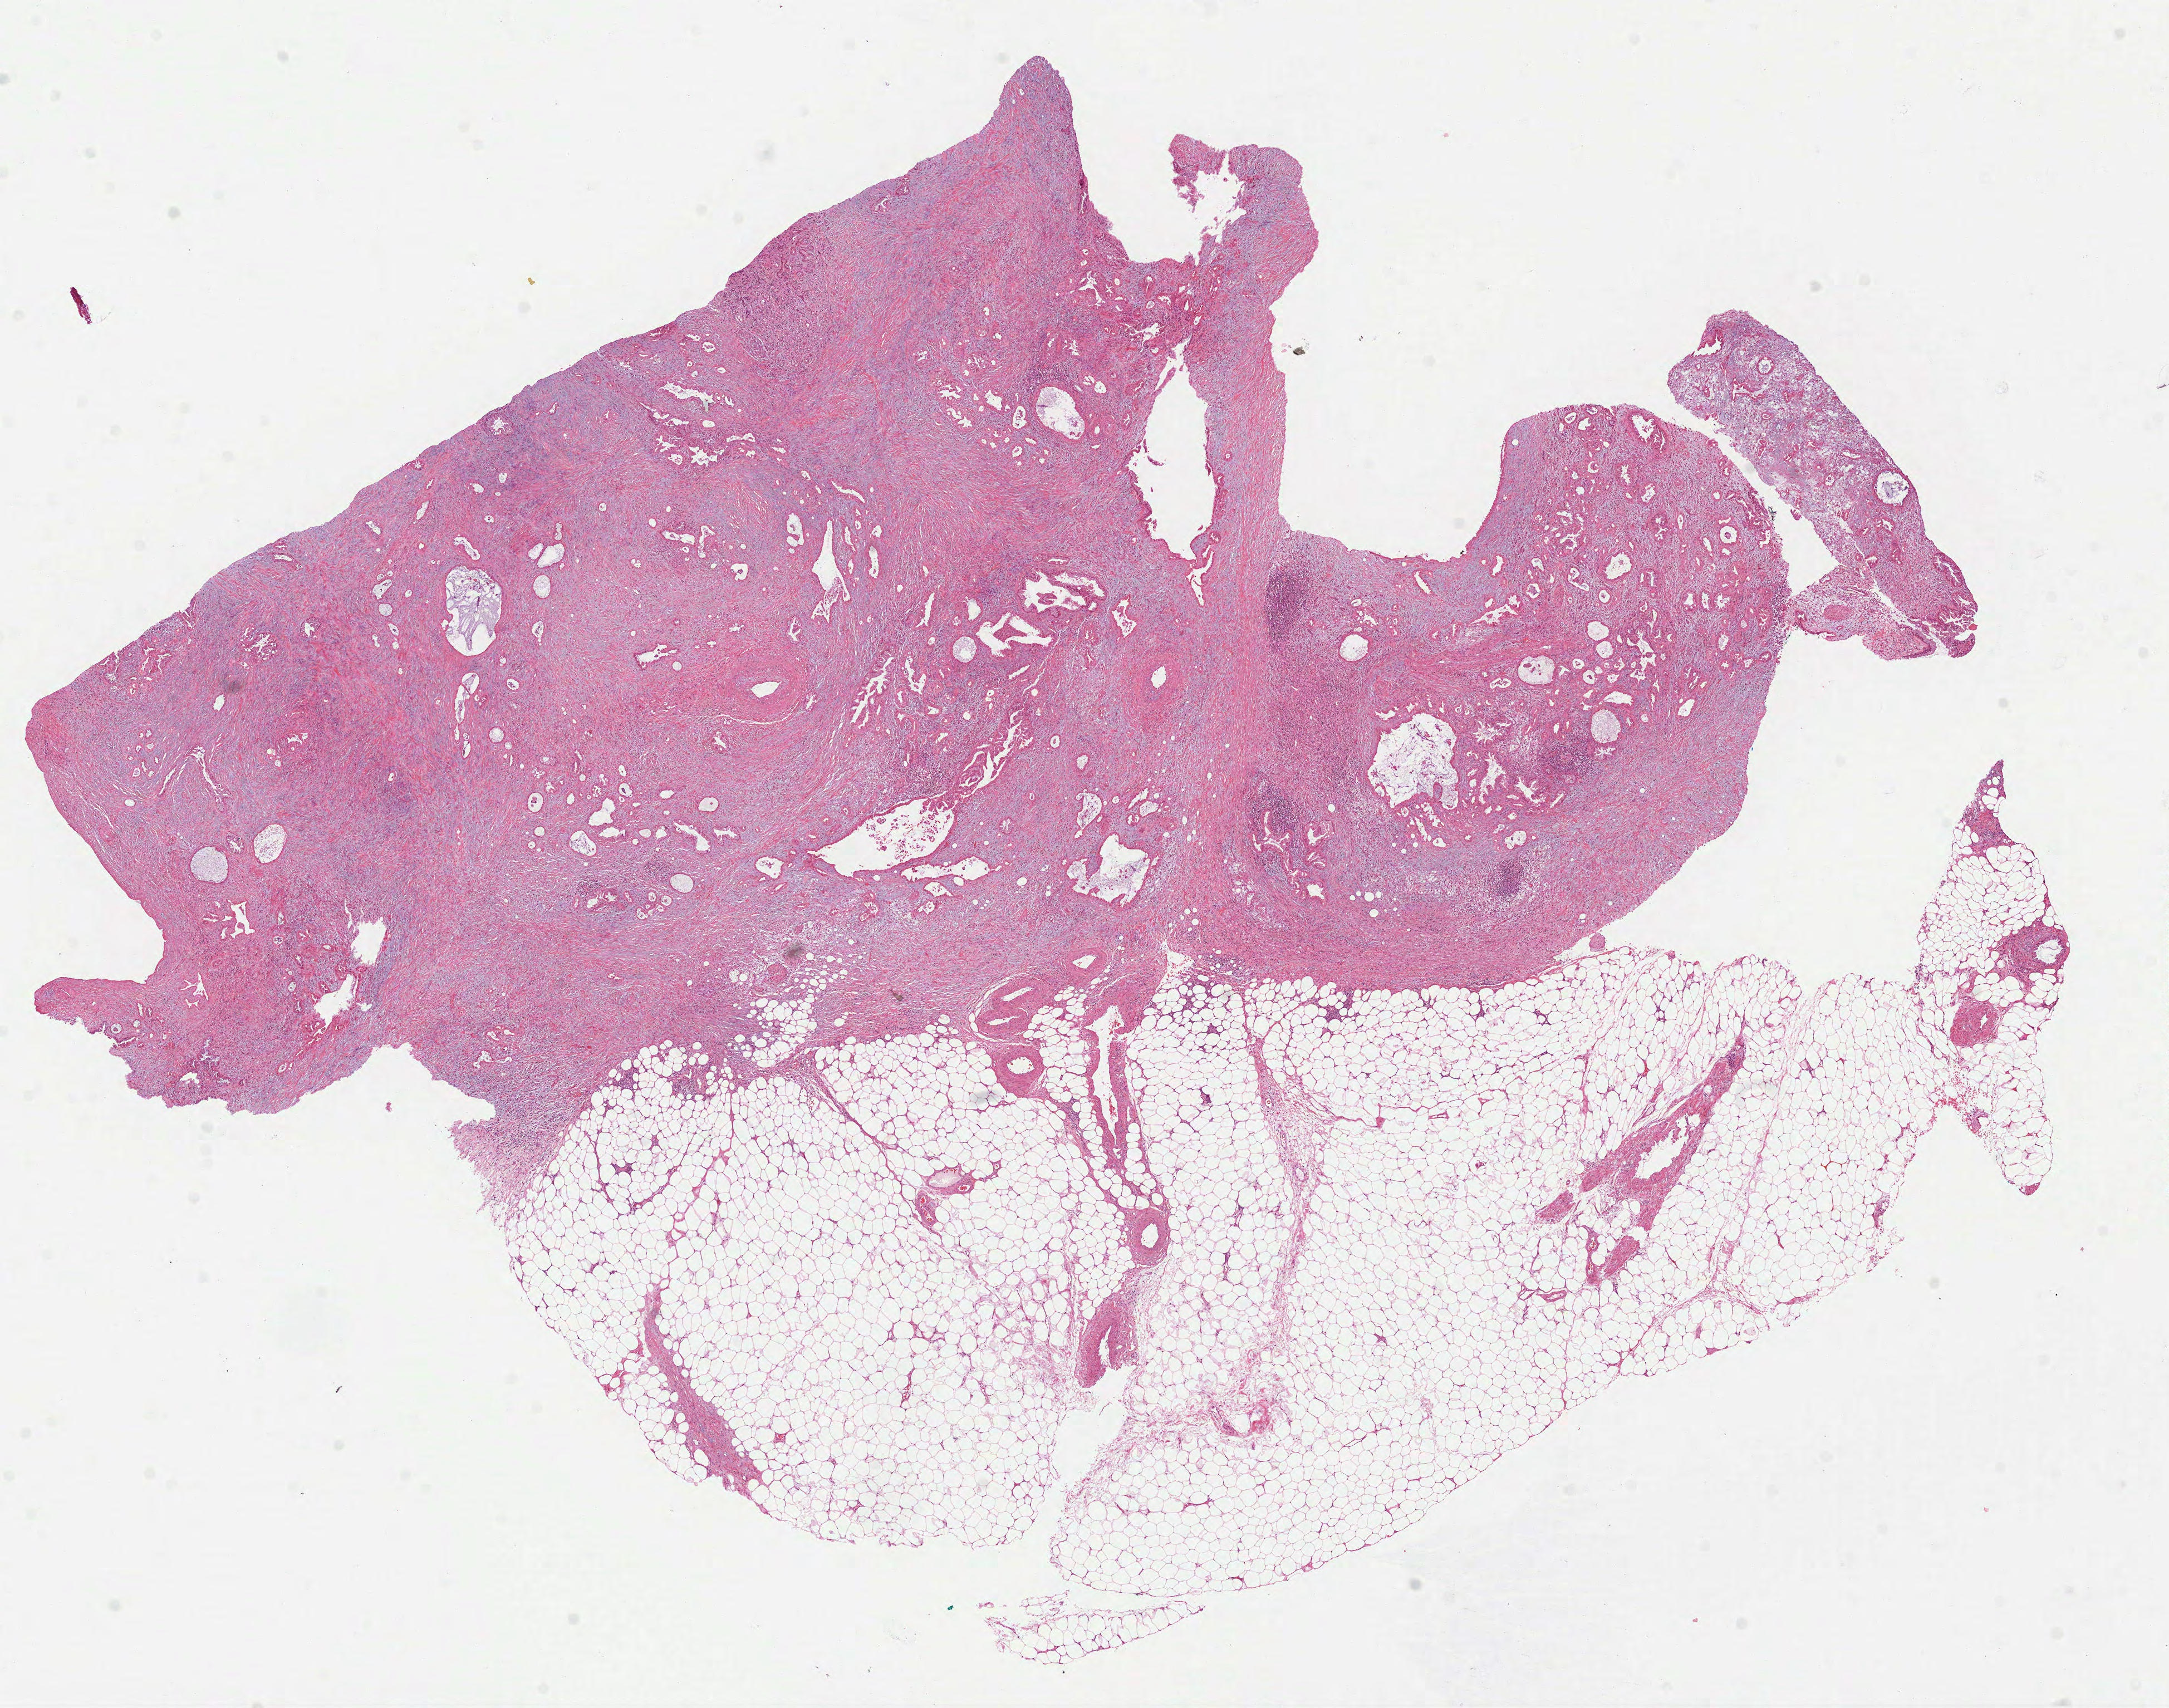
H&E whole-slide image, low-resolution overview of the scanned area, about 15.7 x 12.4 mm (slide scanned at 40x), FFPE section, pancreas, primary tumour sample. Male patient; age at initial diagnosis 77 years. Histologic grade: G2 (moderately differentiated).
Histologic diagnosis: Infiltrating duct carcinoma, NOS (head of pancreas). AJCC pathologic stage: IIB (7th edition).